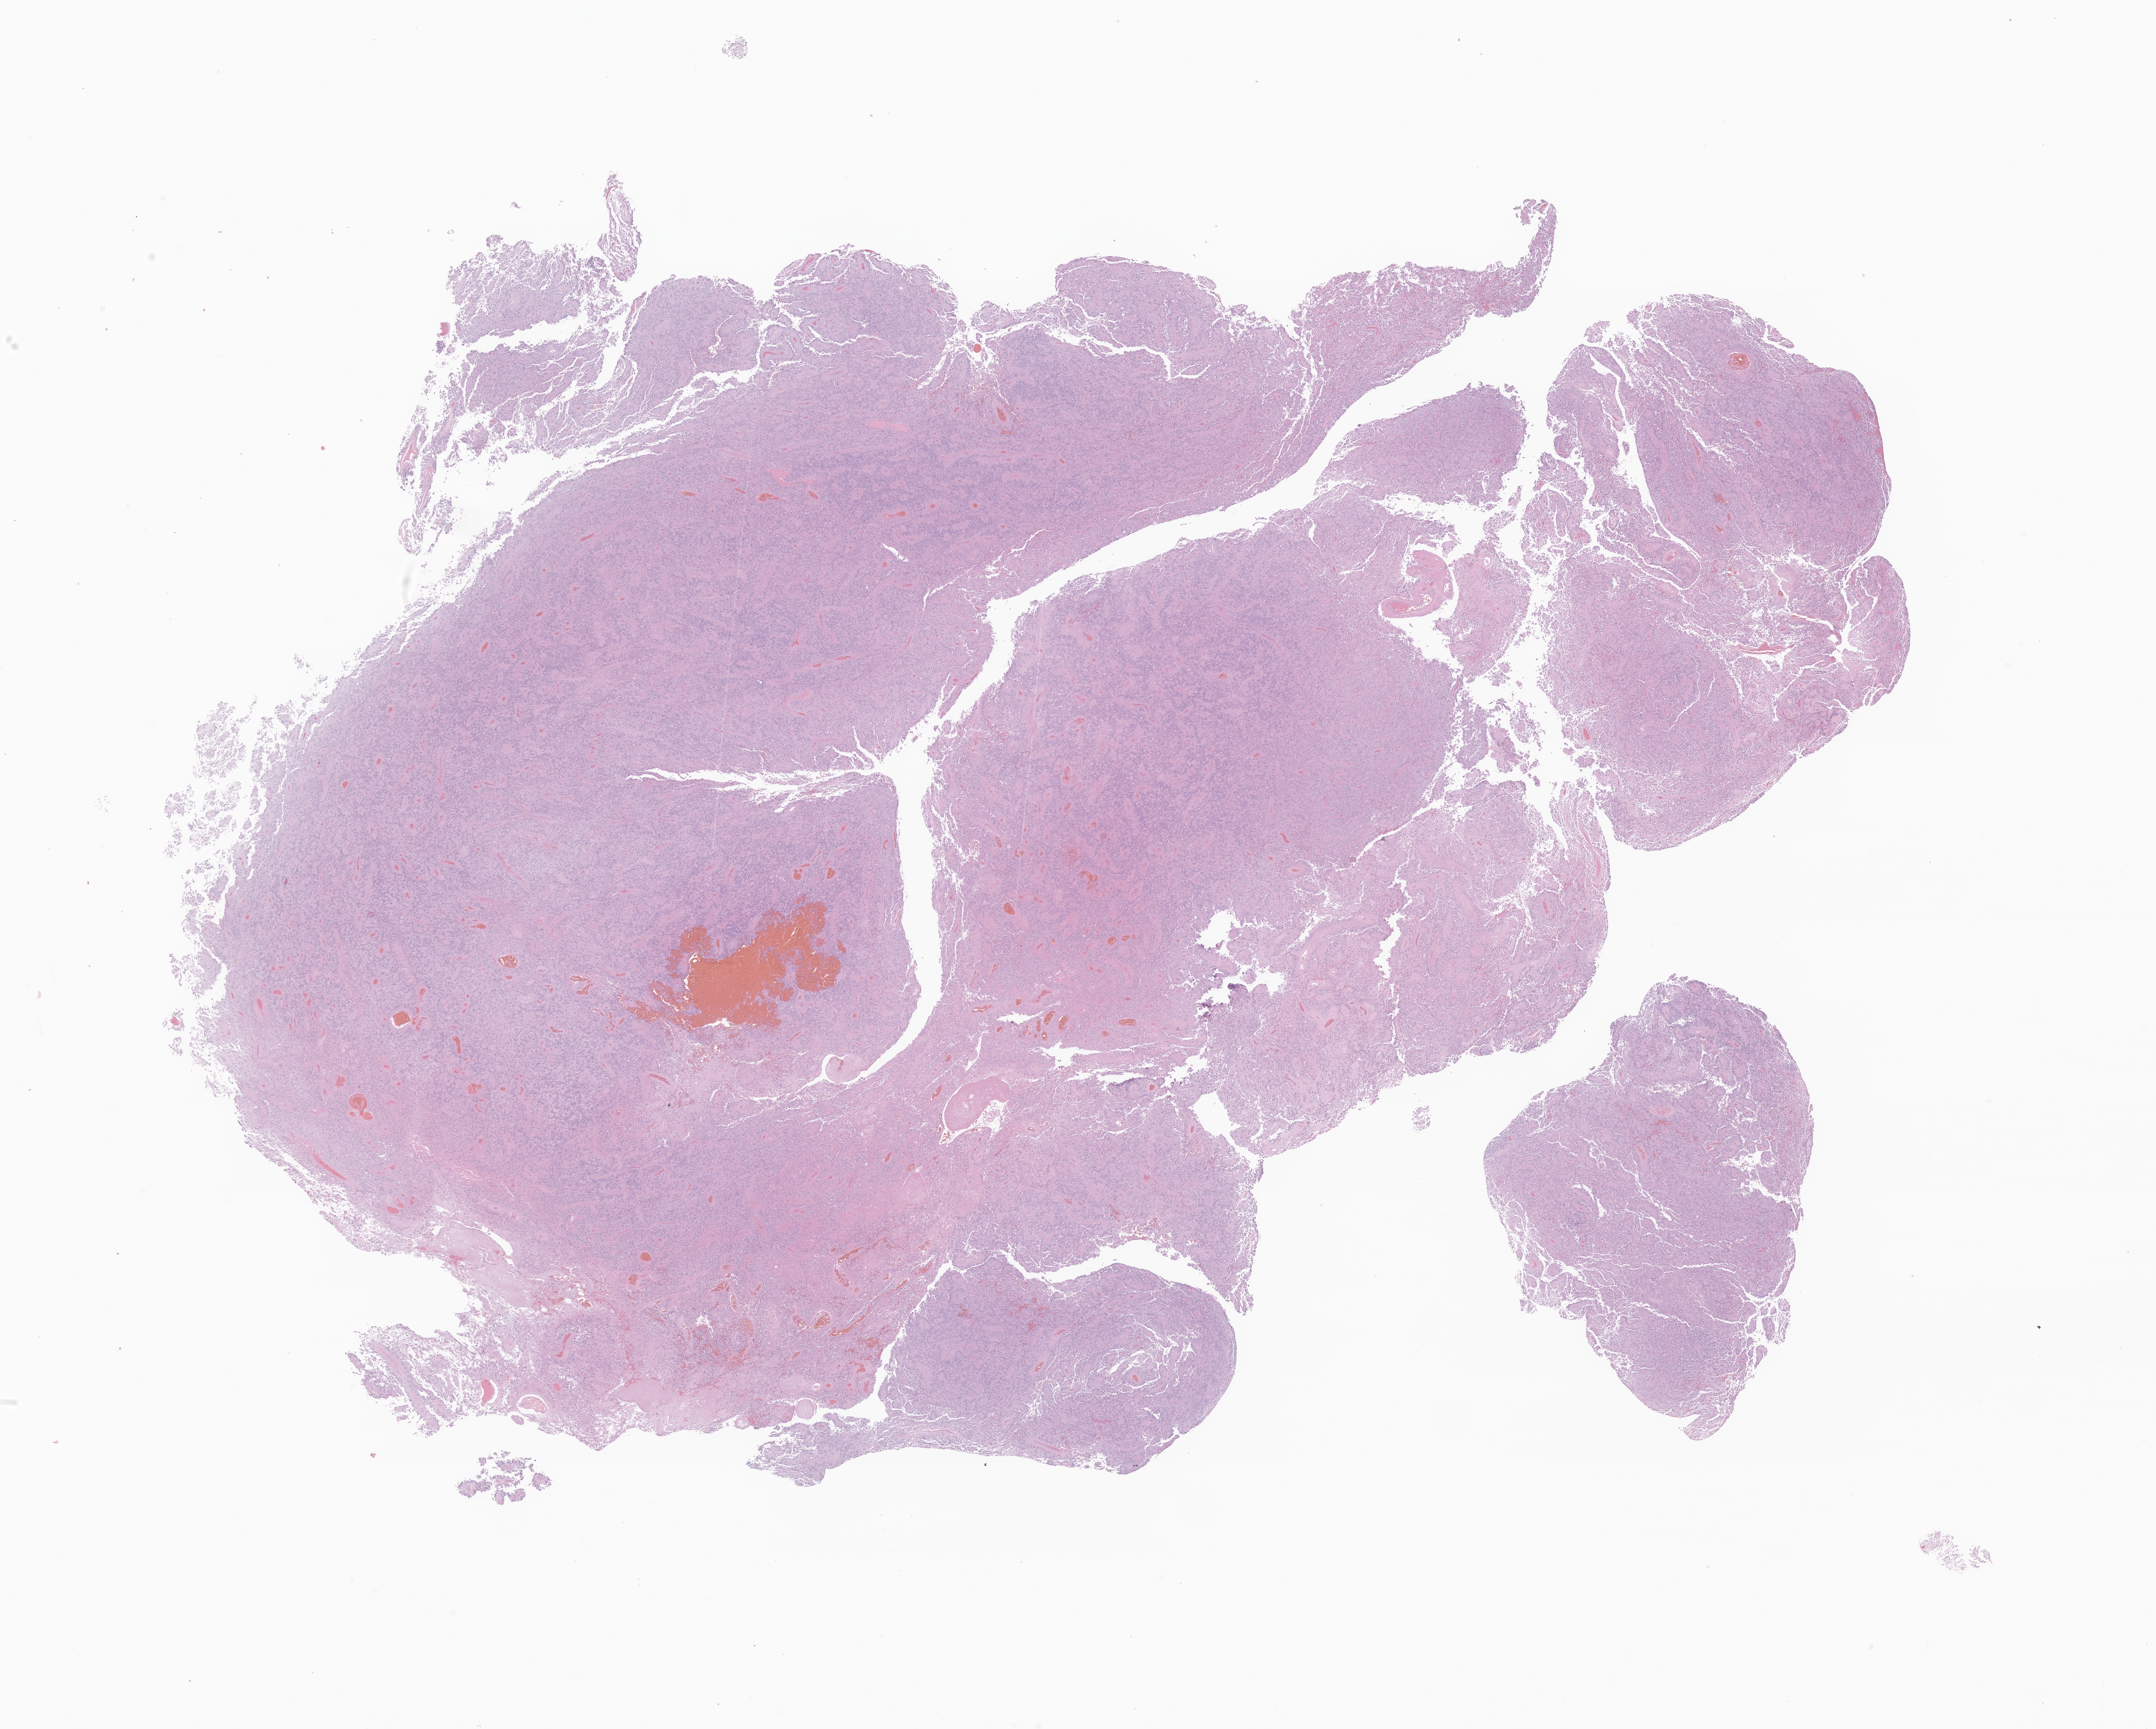
Digitized haematoxylin and eosin-stained section of tumor tissue from the brain — whole scanned area (about 25.5 x 20.4 mm) shown as a low-resolution overview. Formalin-fixed paraffin-embedded section. Patient: female, age 253 months (21 years 1 month).
Diagnosis (ICD-O-3 morphology term): Ependymoma, NOS.